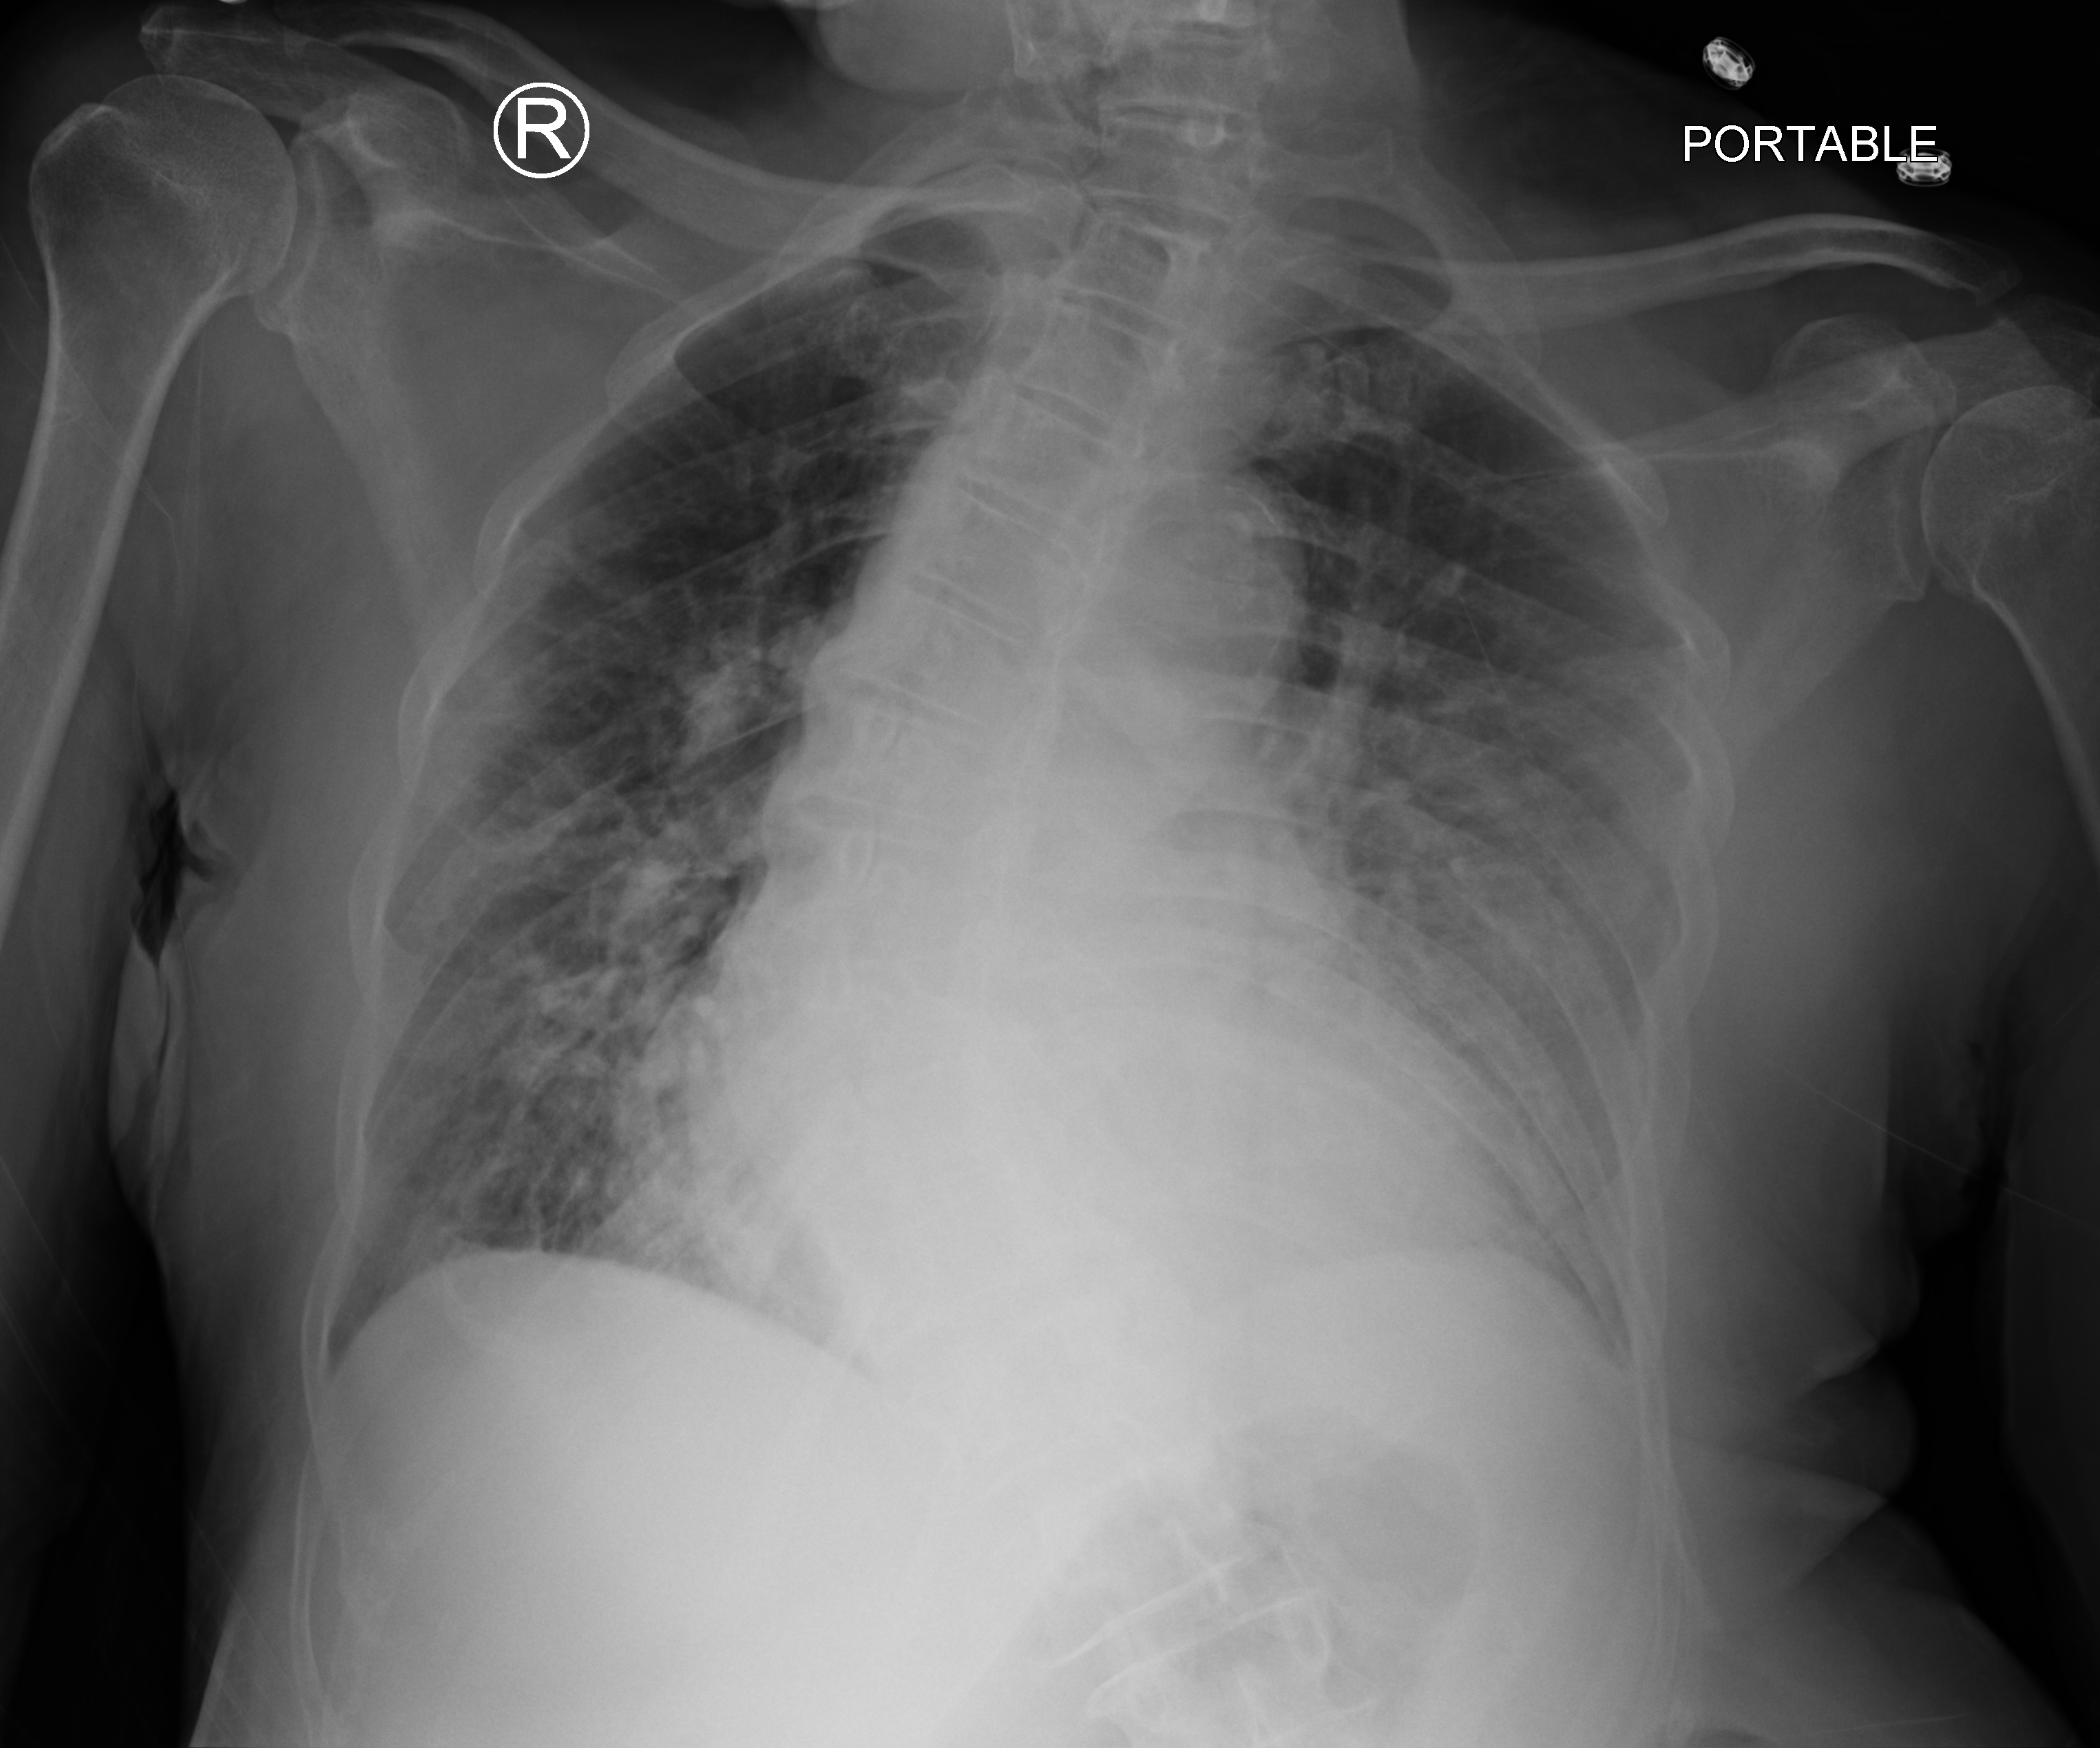
Chest X-ray (portable); anteroposterior (AP) projection. Patient hospitalised with COVID-19; male, aged 75–90 years.
From the hospital-stay record, not from the radiograph (when in the stay this image was taken is not recorded): mechanically ventilated during this hospital stay: no; admitted to intensive care during this hospital stay: no.